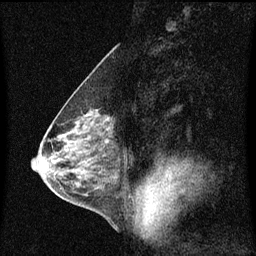
Breast MRI (dynamic contrast-enhanced), one sagittal slice; position 36 of 60 along the scan axis; dynamic contrast-enhanced series, image 2 of 3 at this slice position (ordered by acquisition); 1.5 T; TE 4.2 ms, TR 8.4 ms; 256 × 256 image matrix, field of view 200 × 200 mm. Patient: female, 58 years.
Outlined on this slice (semi-automatically segmented with operator editing):
- analysis volume of interest (the breast-tissue region the enhancement analysis was run in; not a lesion): bounding box (x1, y1, x2, y2) in pixels: (79, 110, 114, 143)
- tumour enhancement mask (voxels above the 70 % enhancement threshold inside the analysis volume of interest): (87, 112, 111, 129)